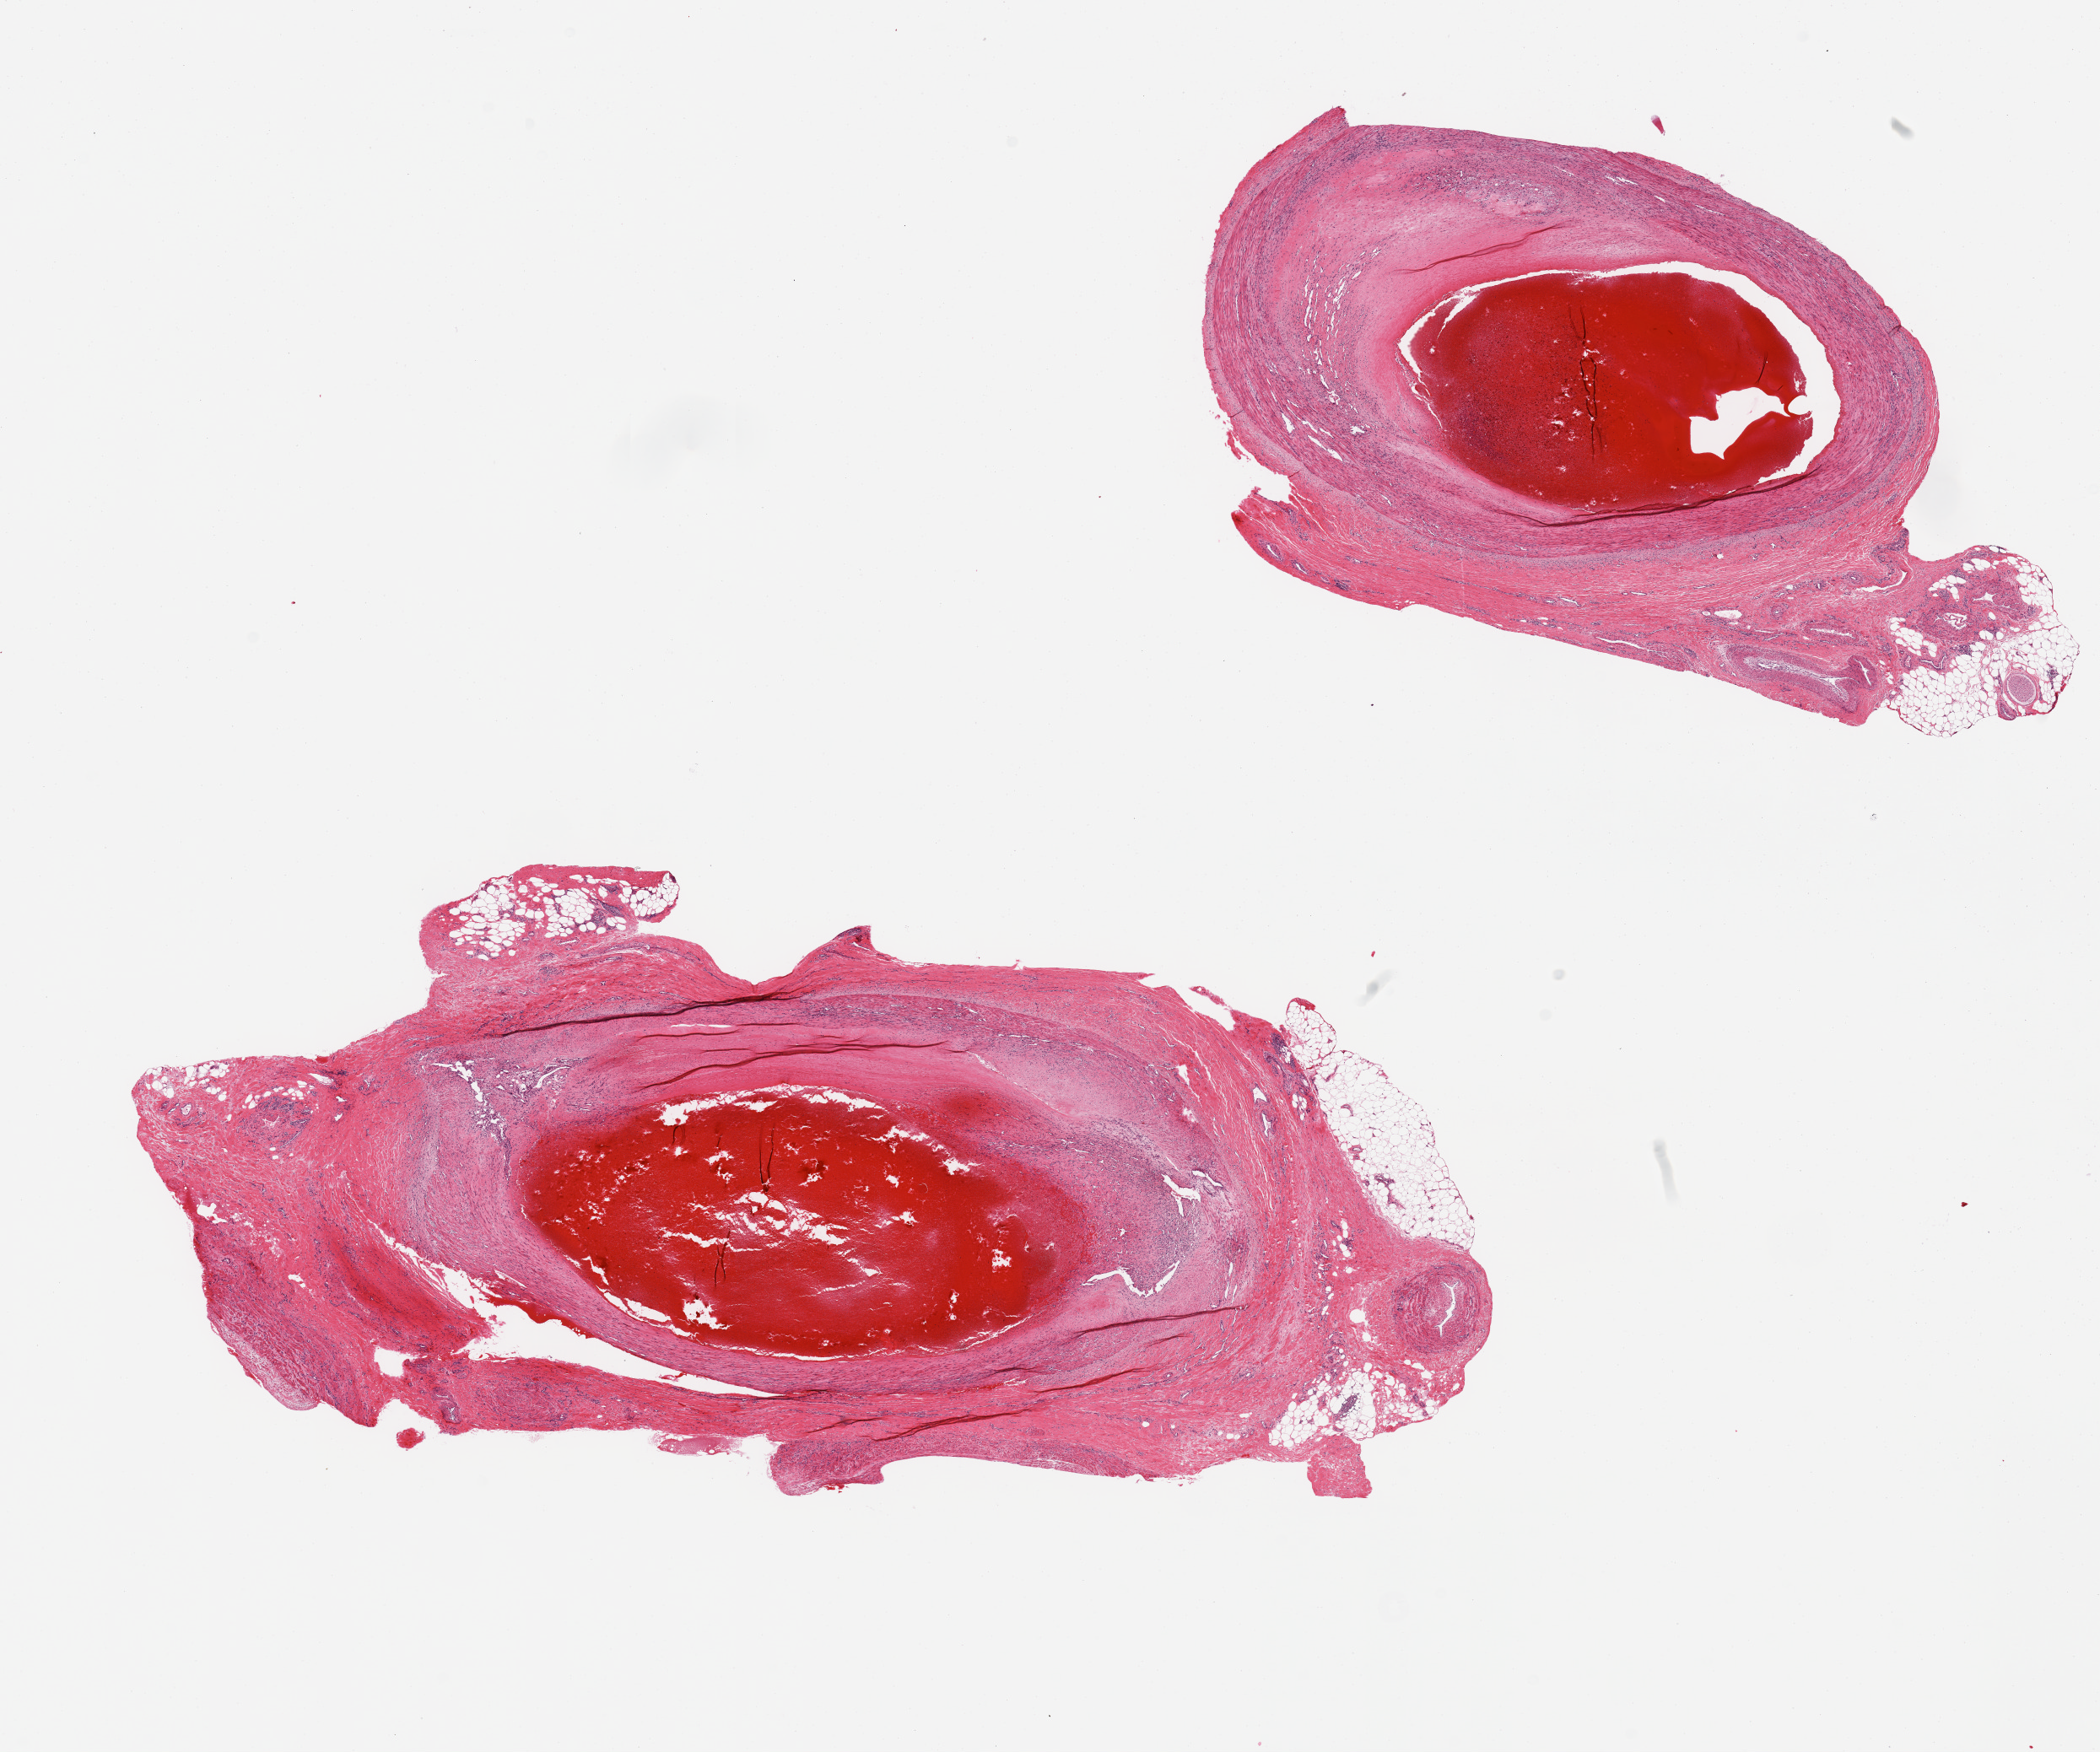
Whole-slide image, H&E stain, brightfield, low-resolution overview of the scanned area, about 19.7 x 16.4 mm, PAXgene-fixed, paraffin-embedded tissue, sampled site (target tissue): tibial artery, donor tissue sample.
Reviewer comment on this tissue sample: 2 pieces, atherosclerotic plaque and organizing thrombus, numerous RBCs, attached portions of fibrous, vascular and adipose tissue.